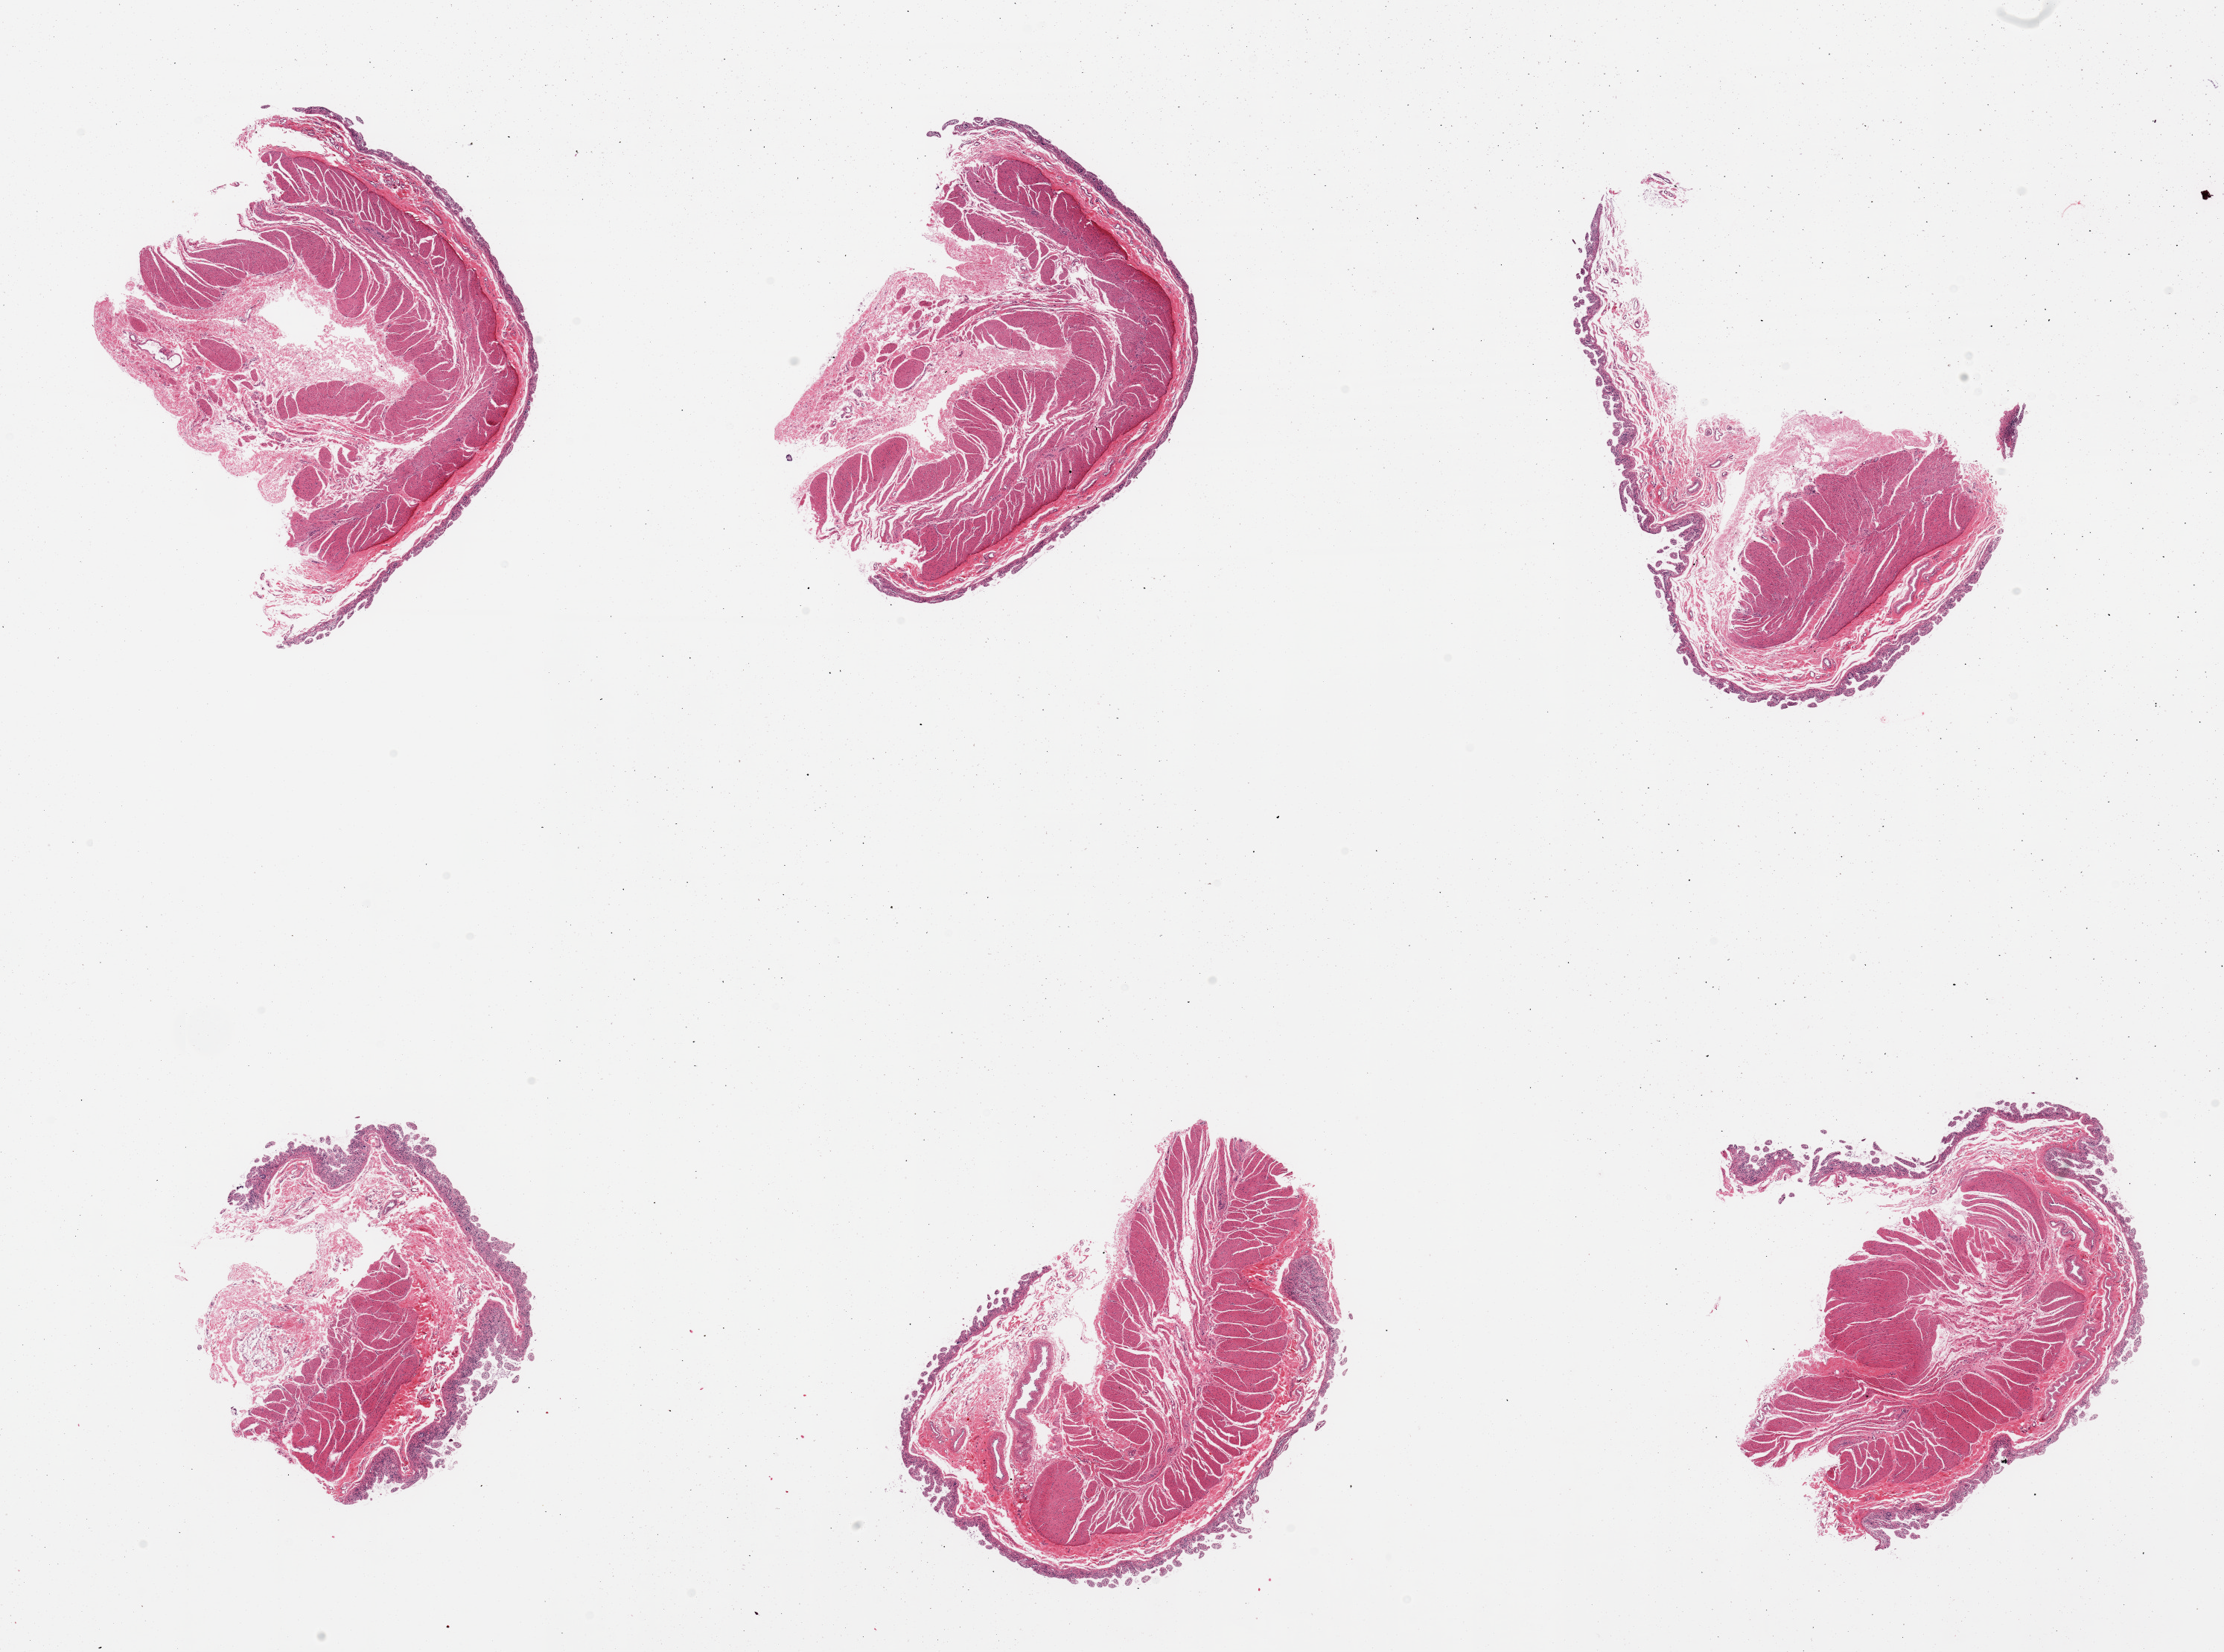
Whole-slide image, H&E stain, whole scanned area (about 23.6 x 17.6 mm, slide scanned at 20x) shown as a low-resolution overview. Donor: male.
Specimen: PAXgene-fixed, paraffin-embedded tissue; sampled site (target tissue): sigmoid colon; tissue donor sample.